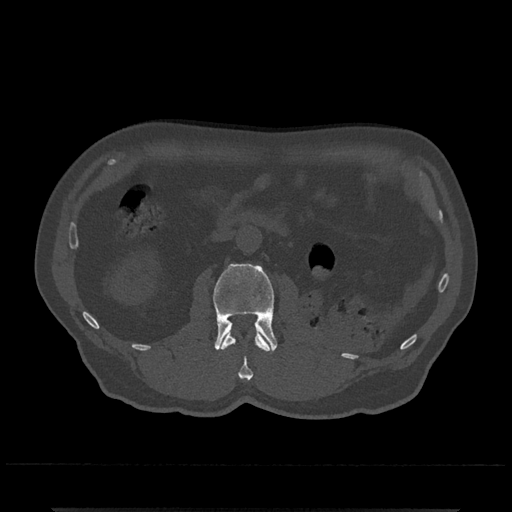
CT including the spine, one axial slice. Position 313 of 797 along the scan axis. Reconstruction kernel Br40s/3. 120 kVp. Bone window (W 1800 / L 400 HU). 512 × 512 image matrix, field of view 393 × 393 mm. Patient: male, 67 years. Case-level facts recorded for this patient, not image findings: primary cancer: prostate.
Structures marked on this image (semi-automatically segmented with operator editing):
- L1 vertebra: bounding box <221,330,270,380> (left, top, right, bottom; pixels)
- L2 vertebra: <213,263,278,352>